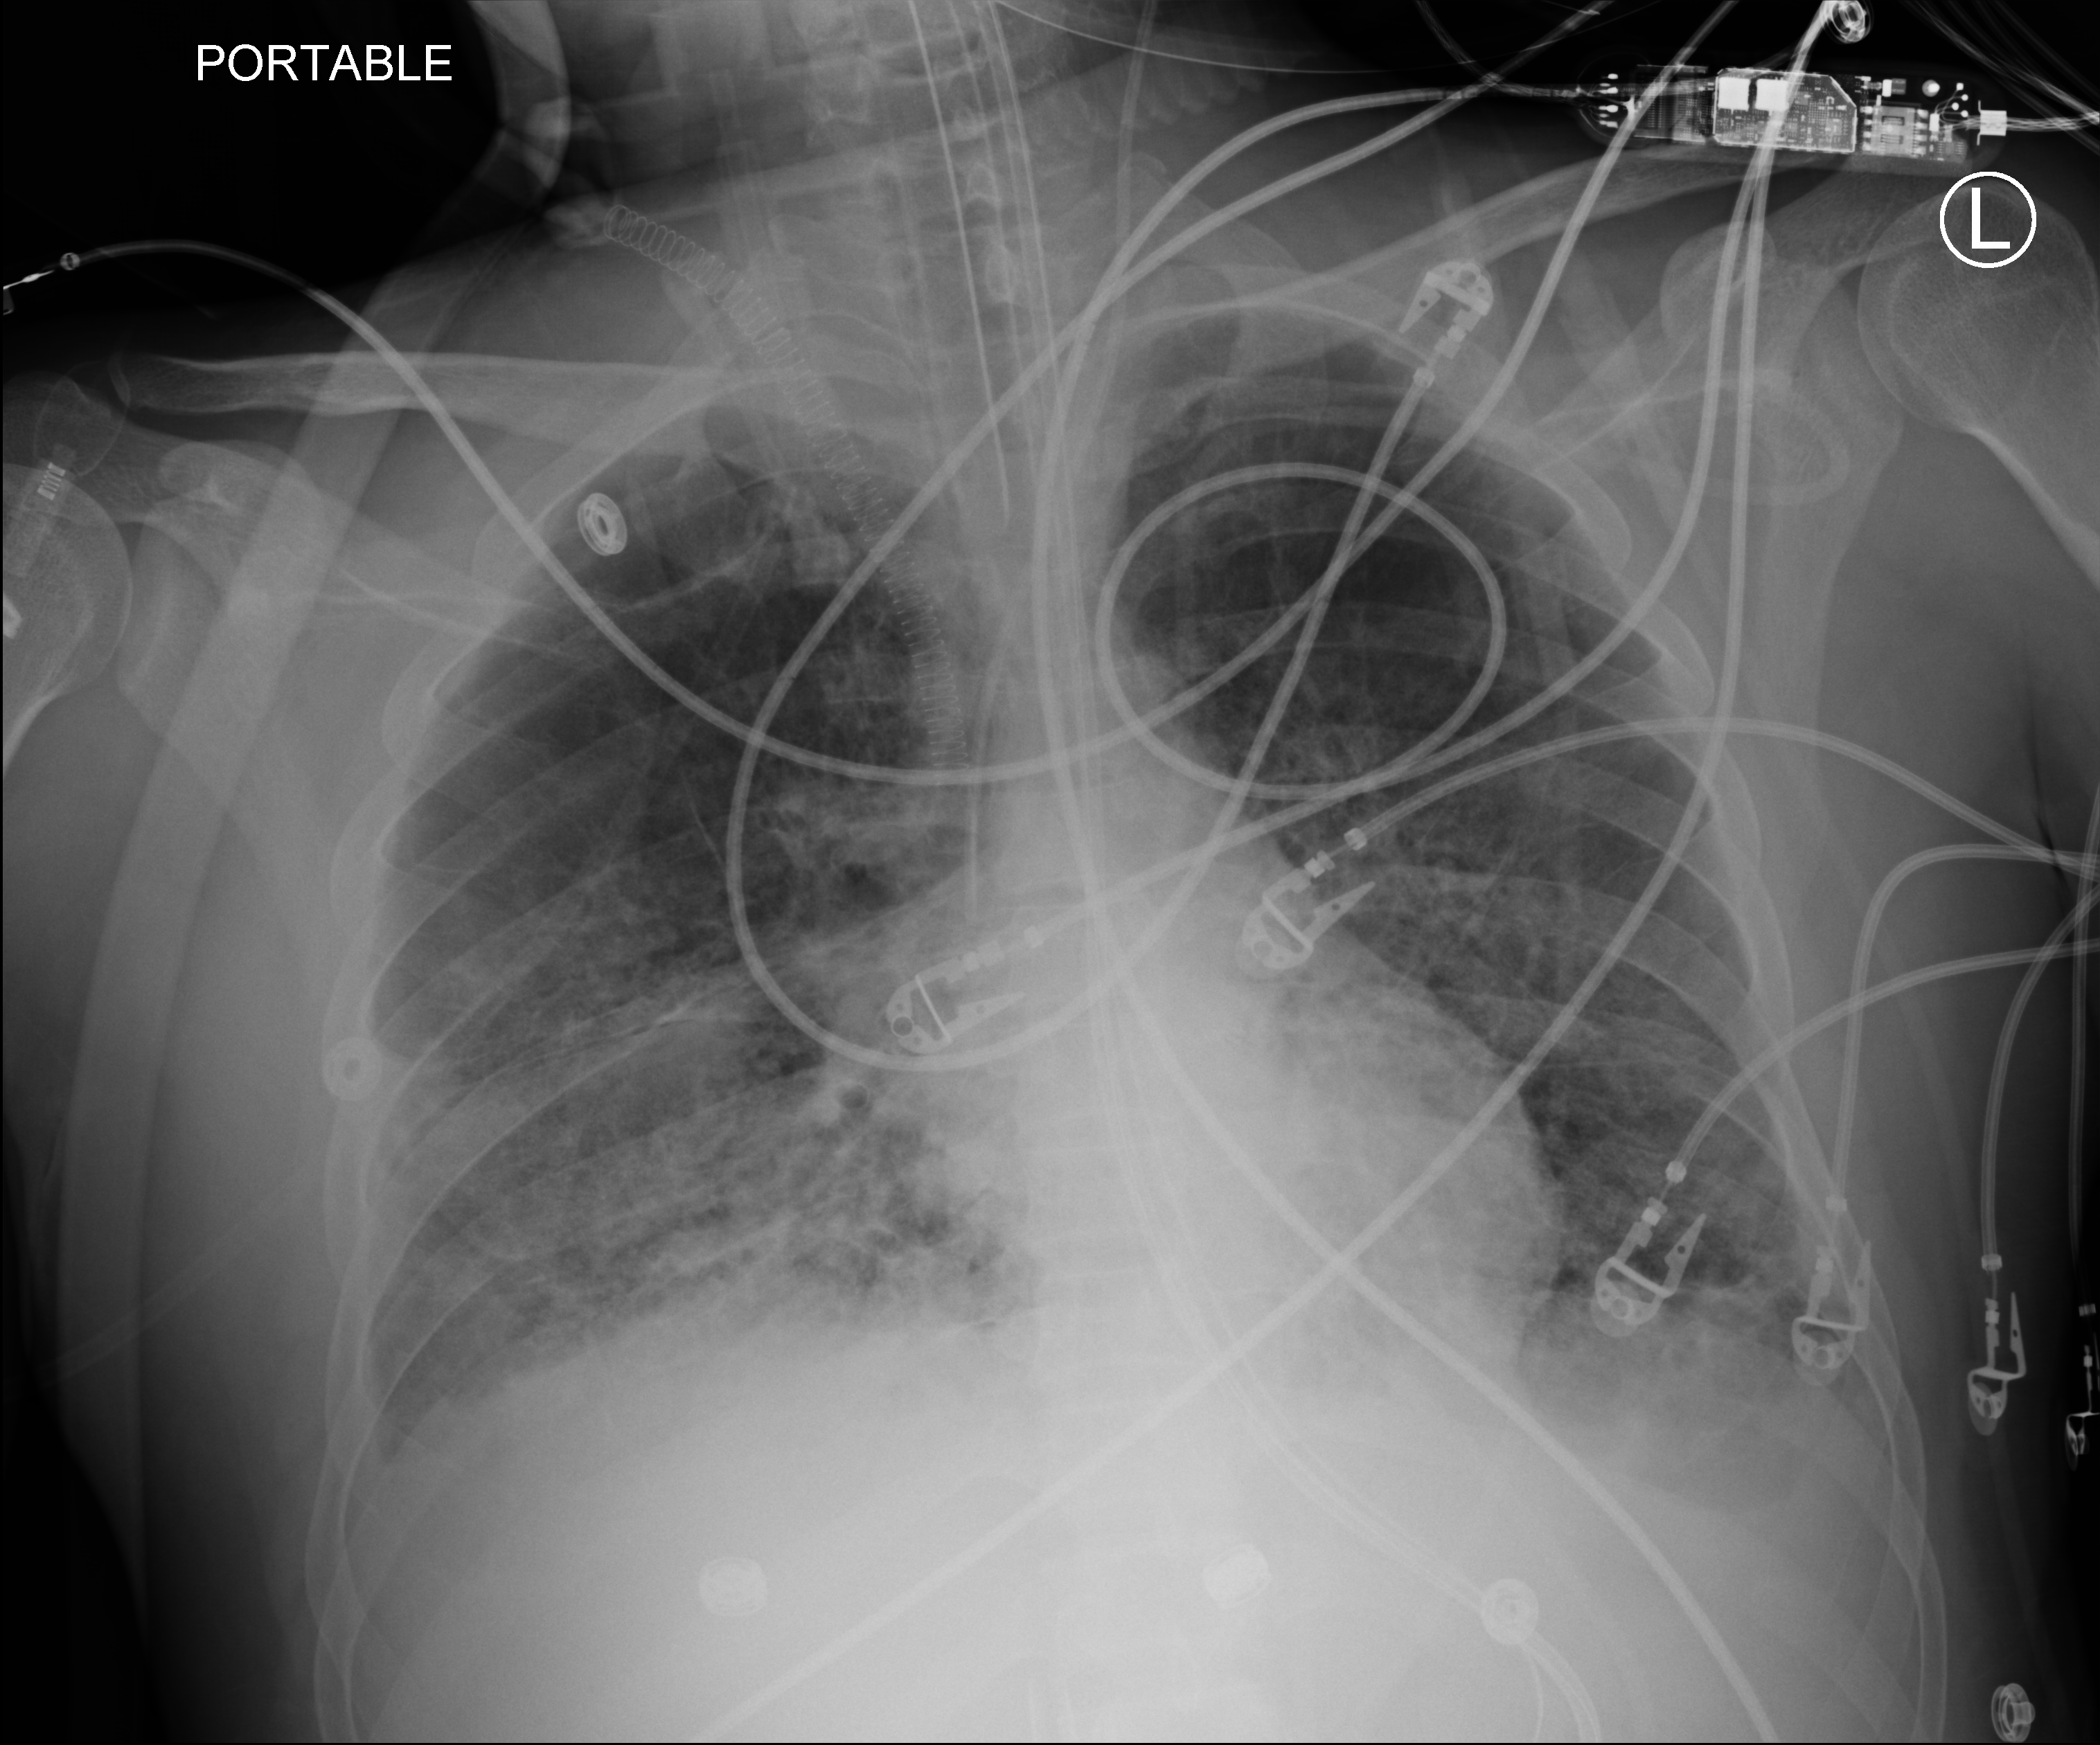
Chest X-ray (portable); anteroposterior (AP) projection. Adult patient hospitalised with COVID-19, age 18–59 years.
Hospital-stay facts (about this admission, not read from this image; timing relative to this image not recorded):
- hypertension (admission record): no
- length of hospital stay: 60 days